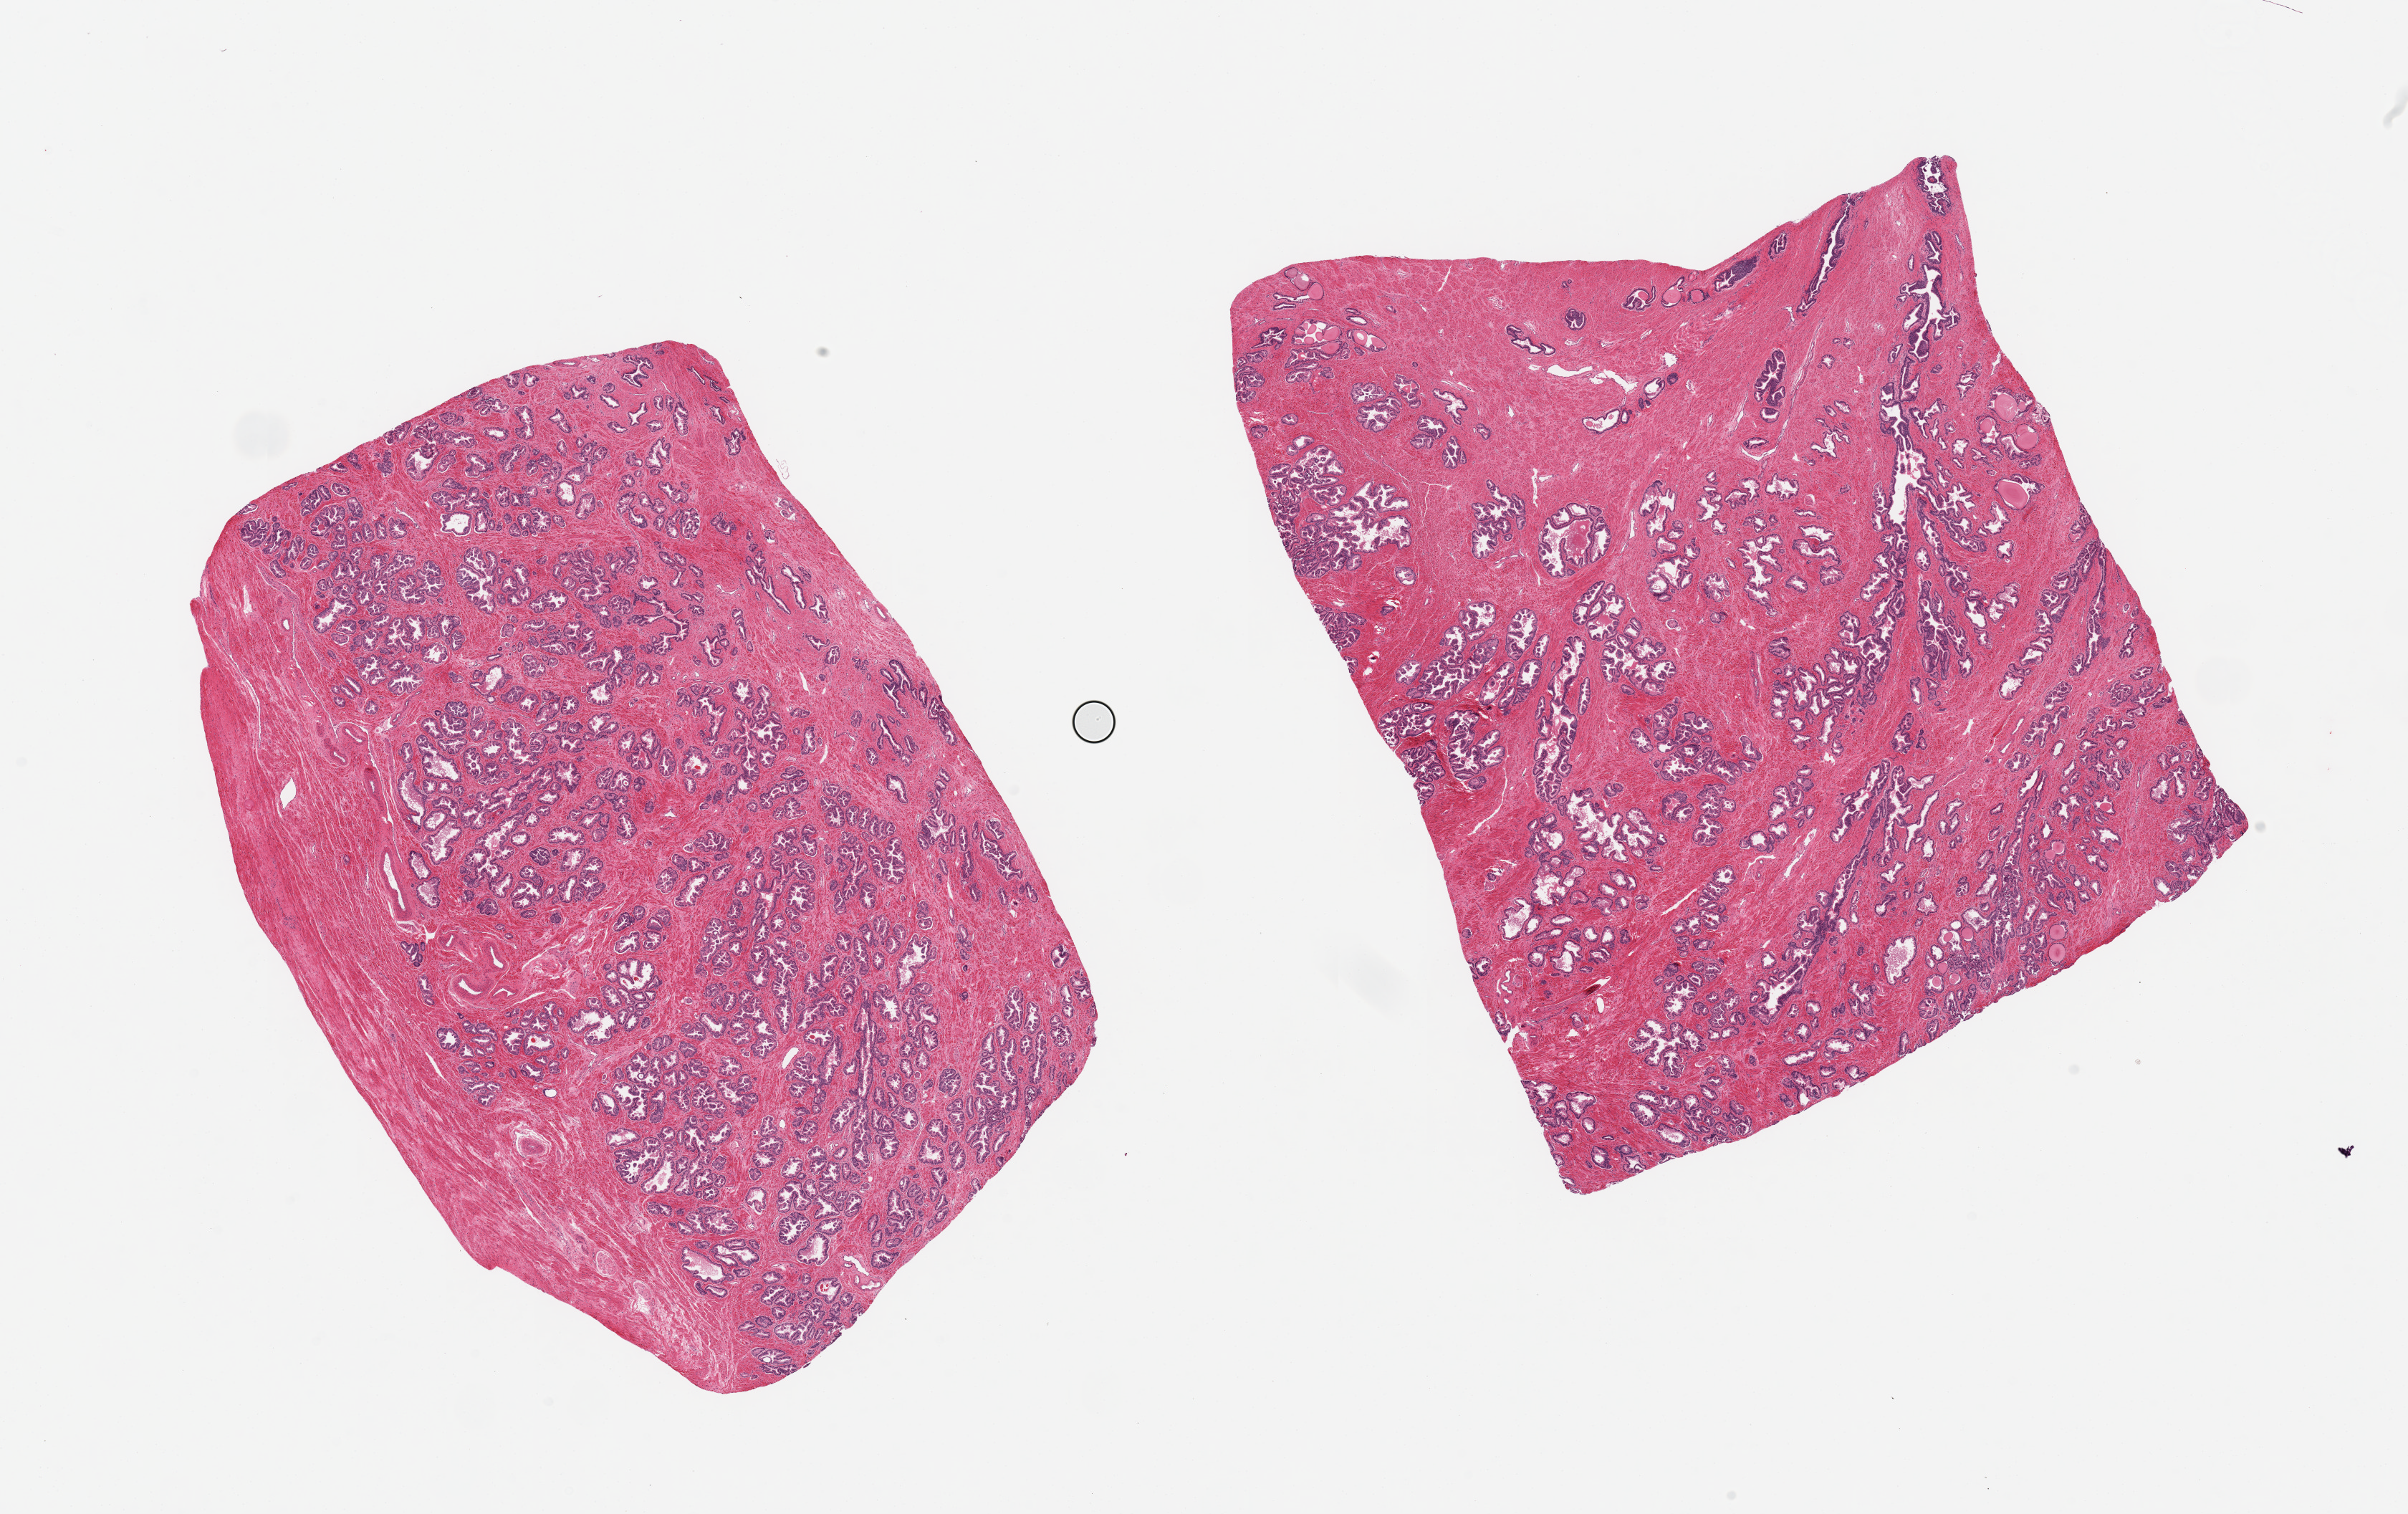
Hematoxylin and eosin (H&E) whole-slide image, a low-resolution overview of the entire scanned area, about 26.6 x 16.7 mm (slide scanned at 20x). PAXgene-fixed paraffin-embedded (PFPE) section. Sampled site (target tissue): prostate. Tissue donor sample. Donor: male.
Reviewer comment on this tissue sample: 2 pieces, no abnormalities.